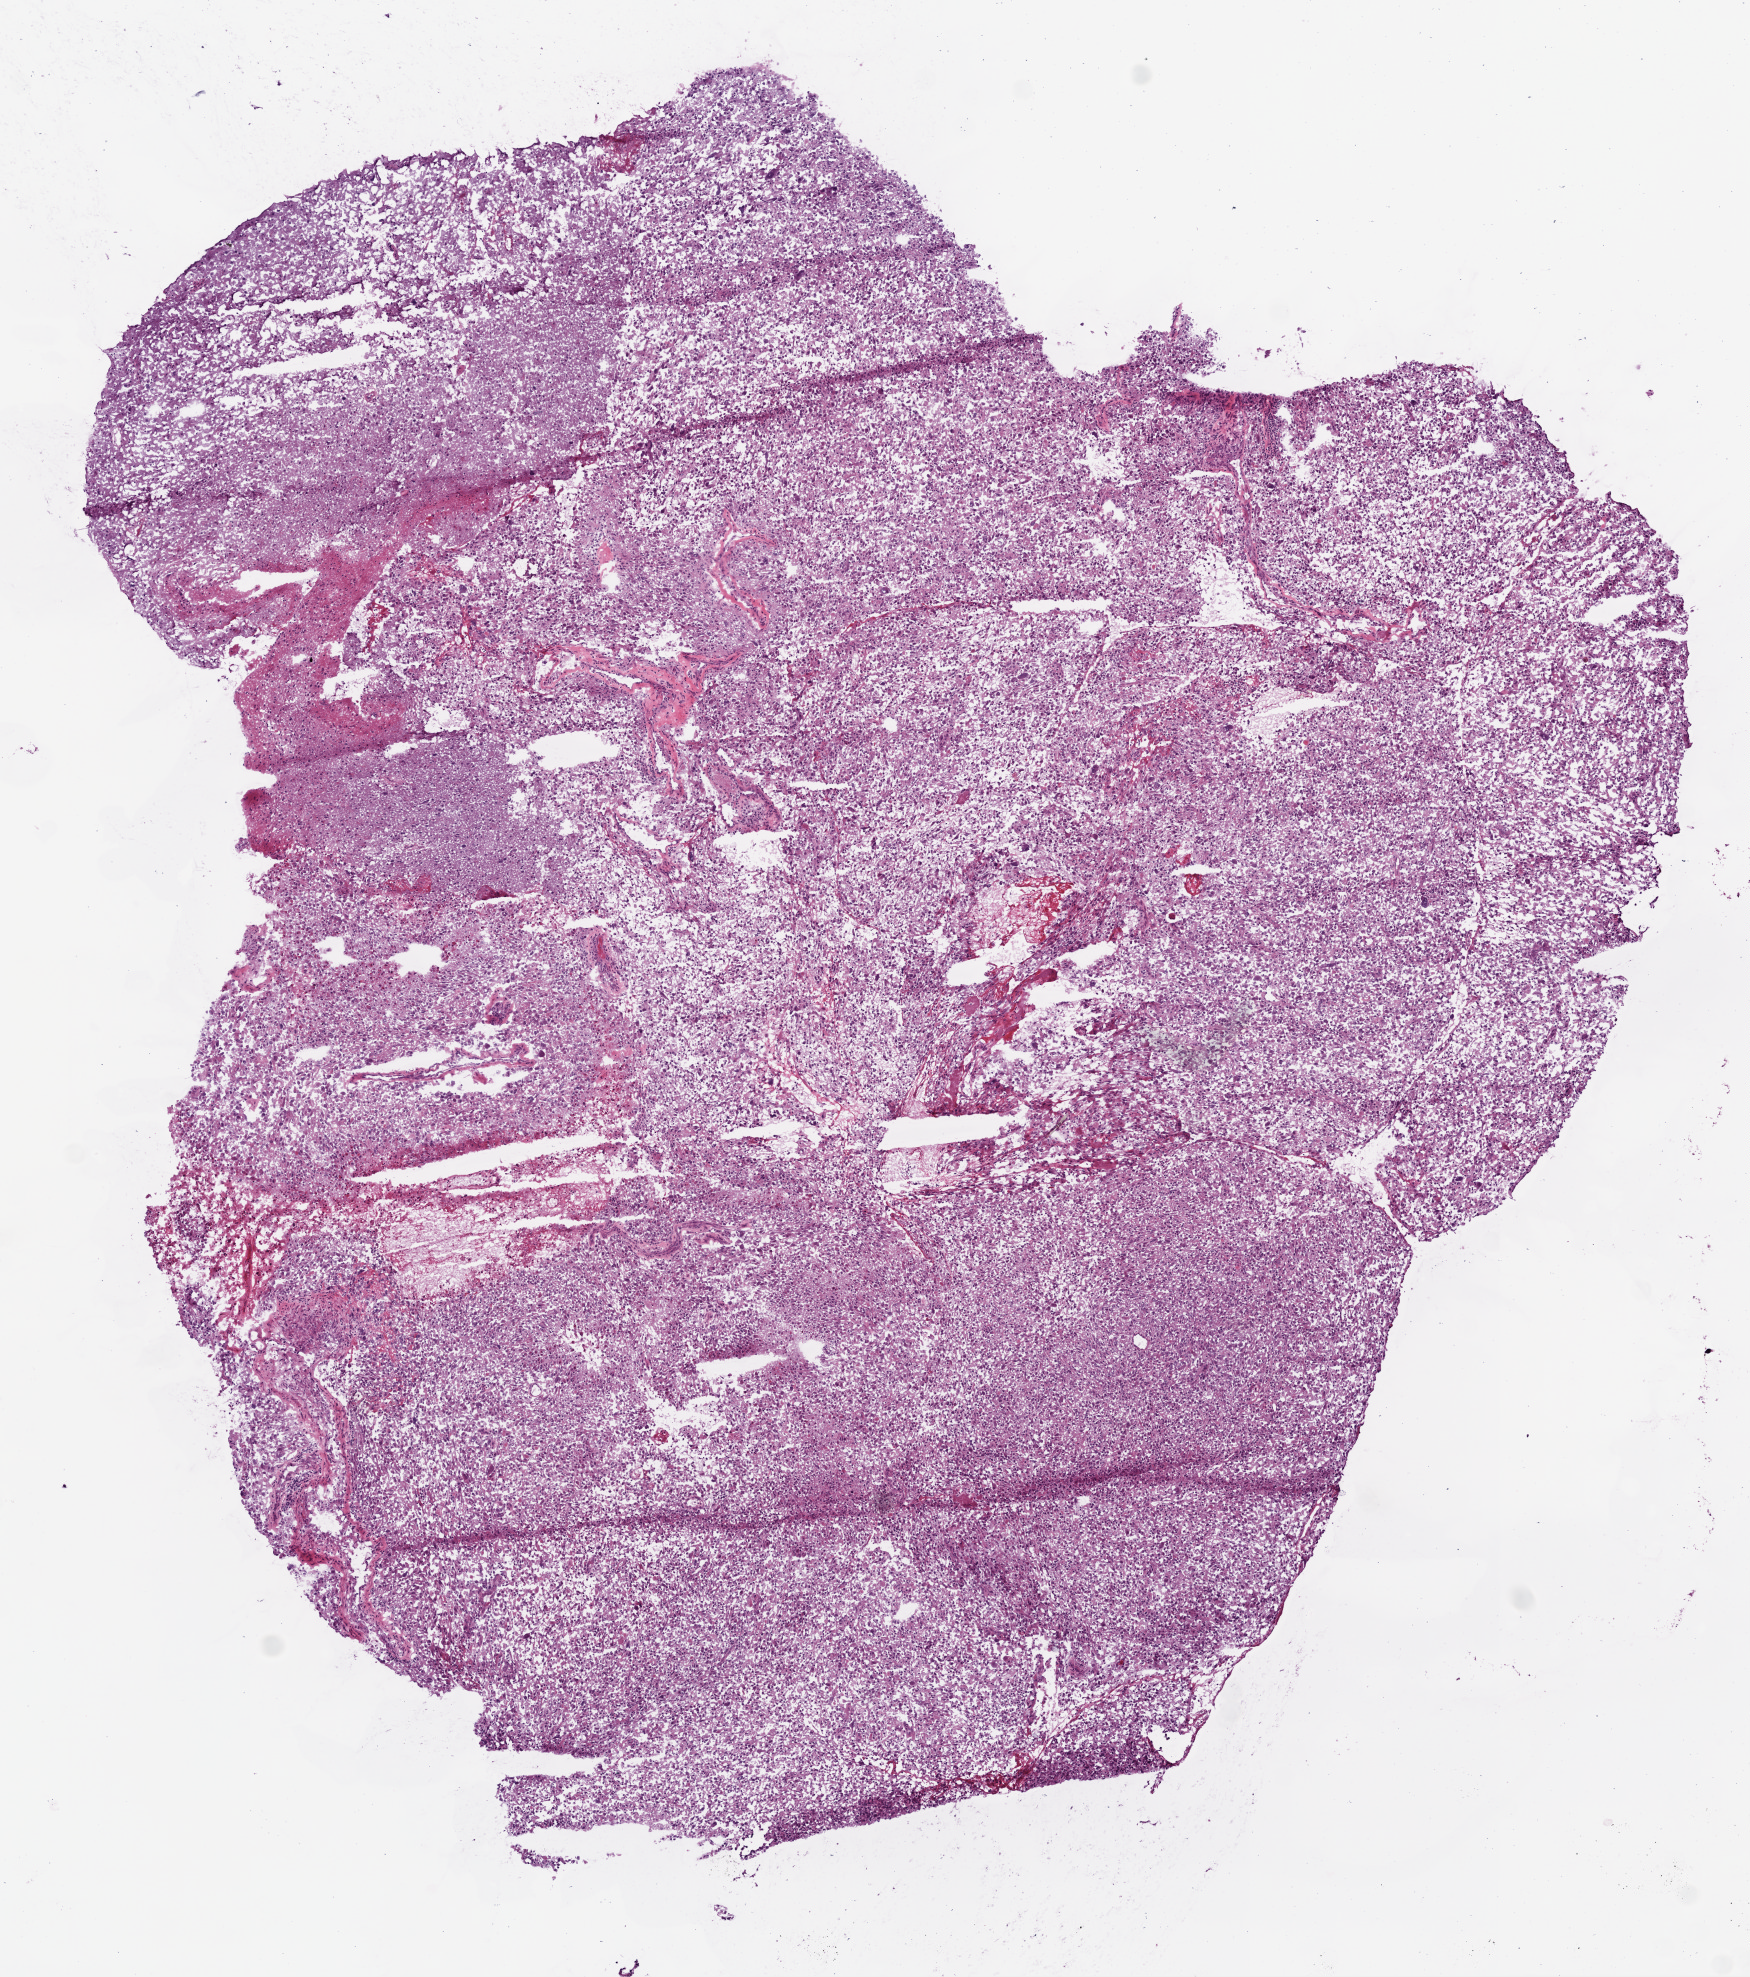
Hematoxylin and eosin (H&E) stained whole-slide image, shown as a low-resolution overview of the whole scanned area (about 7.0 x 7.9 mm, slide scanned at 20x). Frozen section. Primary tumour sample from the brain. Male patient; age at initial diagnosis 40 years. Pathologist review of this section (percent, as recorded): tumour cells 97%, tumour nuclei 85%, normal cells 0%, stromal cells 0%, necrosis 3%.
Diagnosis: Glioblastoma.